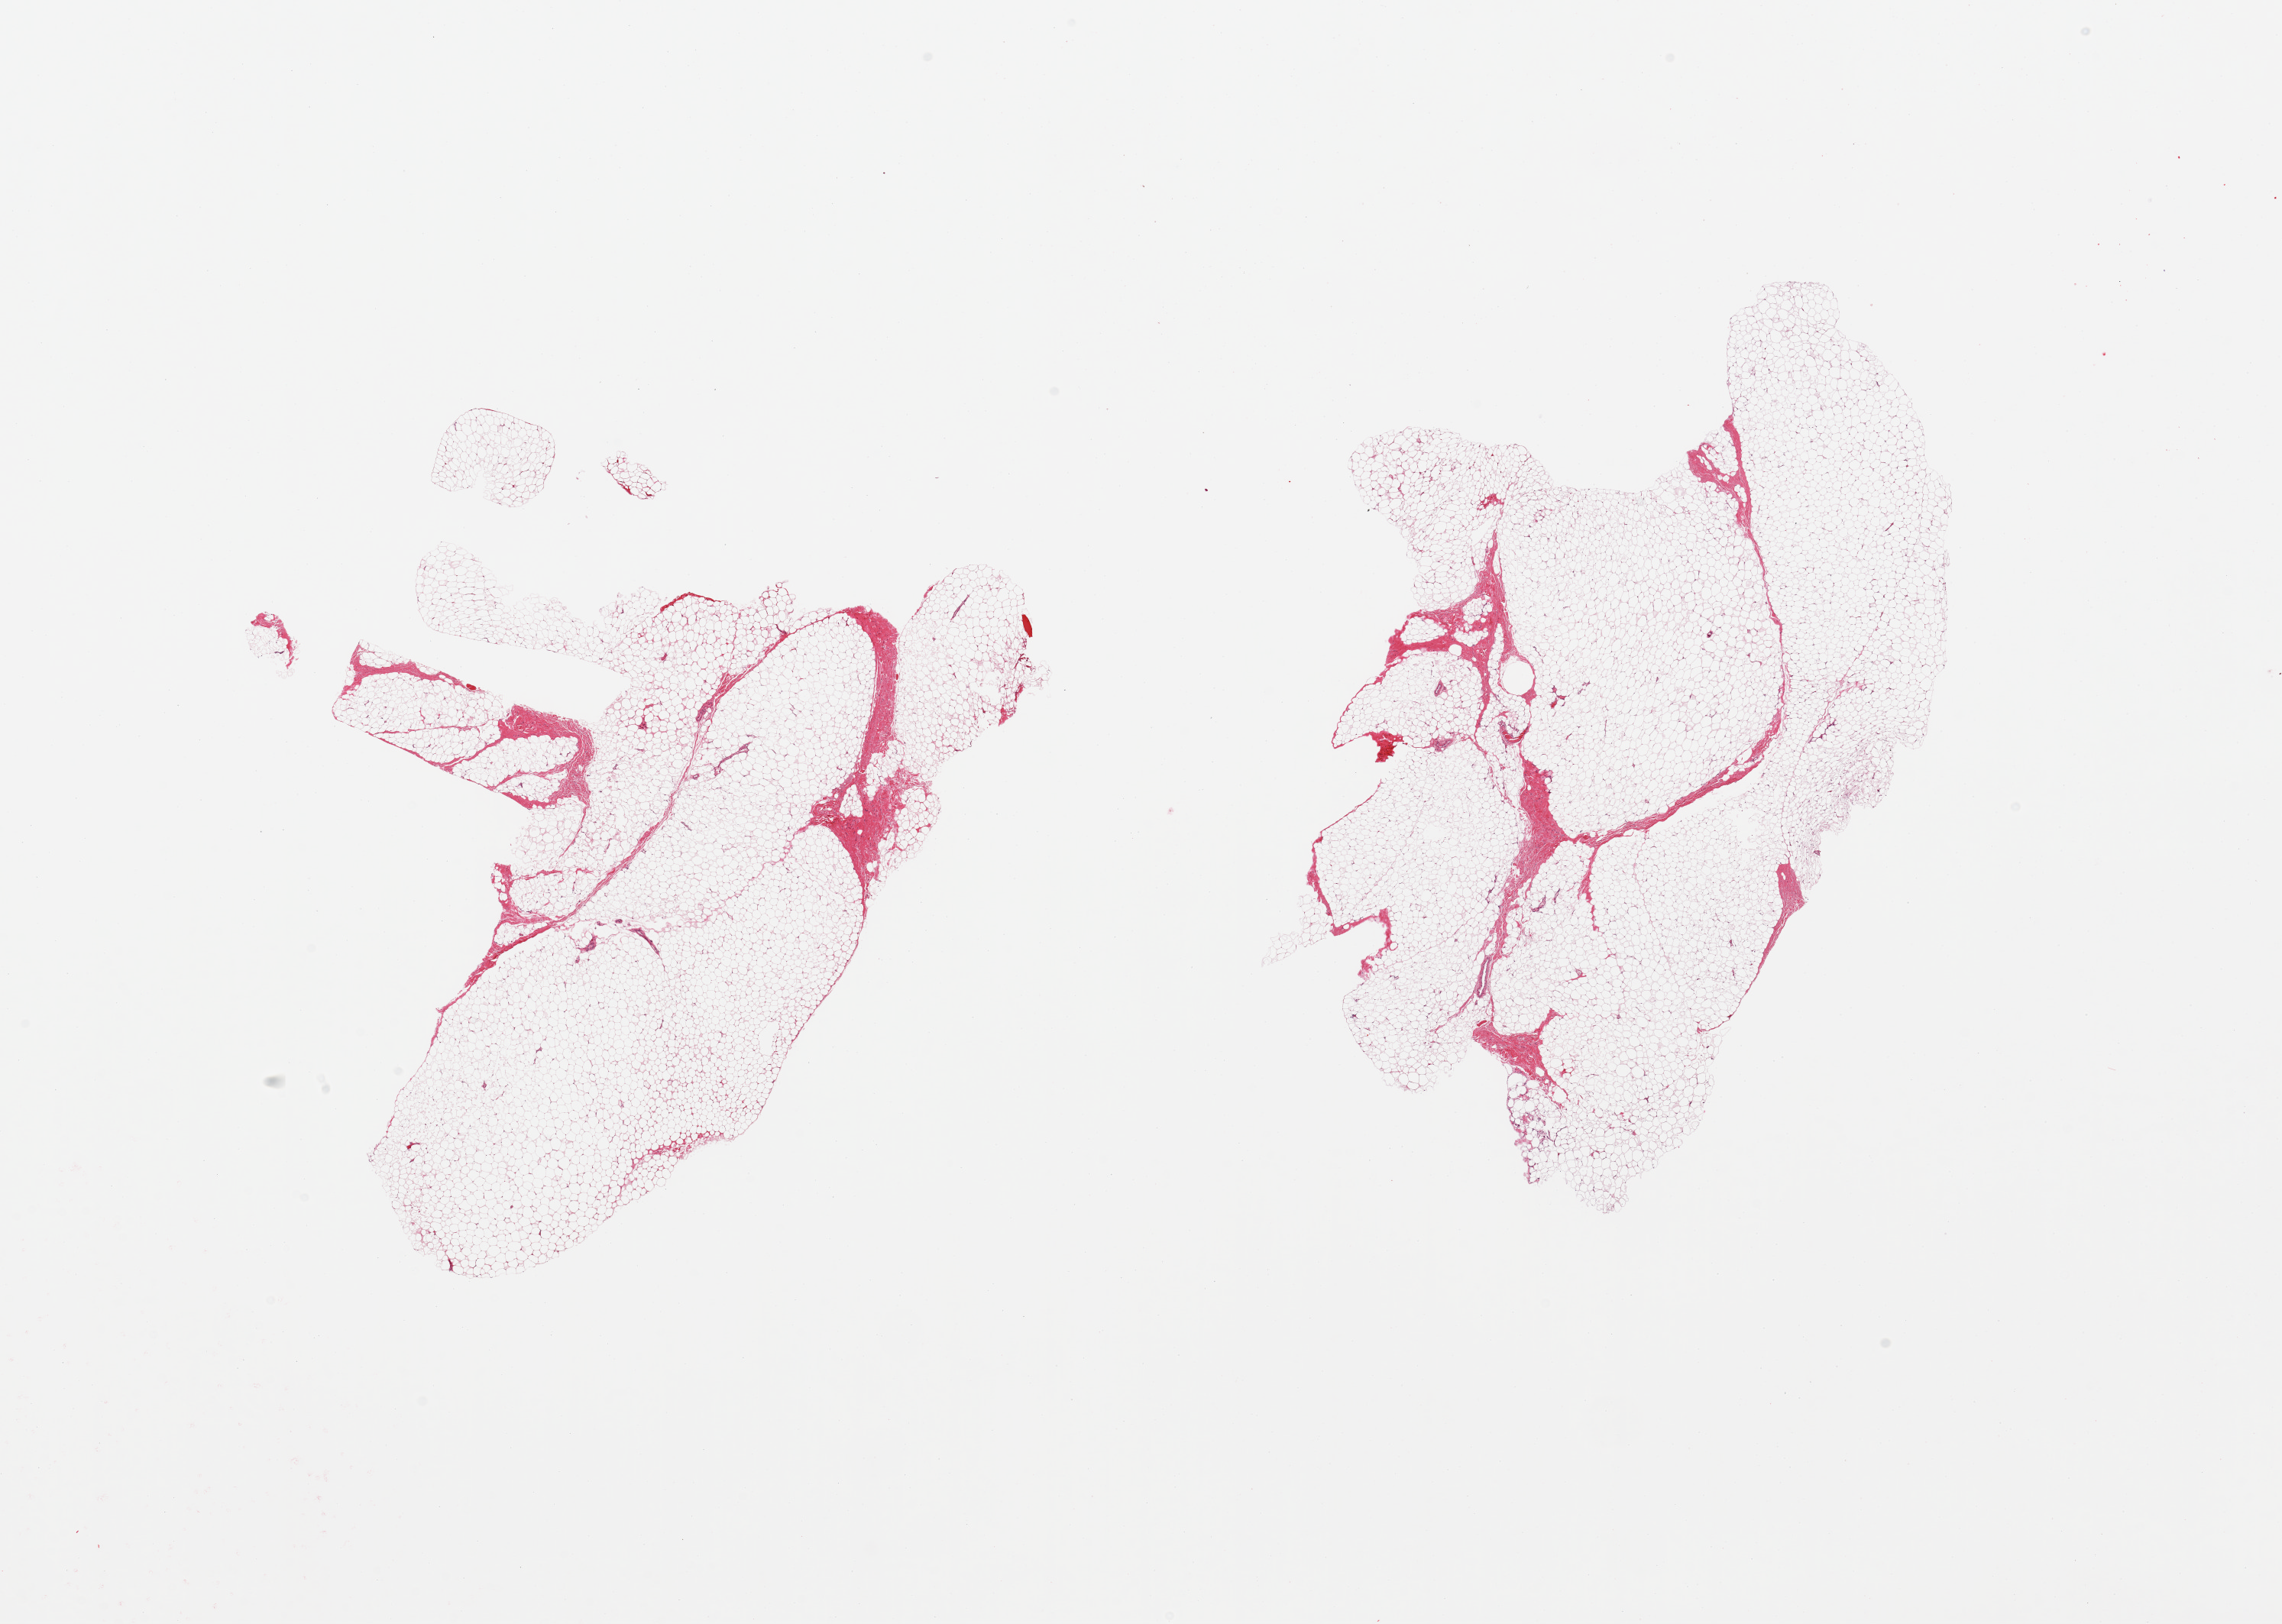
Whole-slide image, hematoxylin and eosin (H&E) stain, low-resolution overview of the scanned area, about 23.6 x 16.8 mm (slide scanned at 20x). PAXgene-fixed, paraffin-embedded tissue. Section of breast (target tissue). Tissue donor sample. Male donor.
Reviewer comment on this tissue sample: 2 pieces; fat with no ducts.